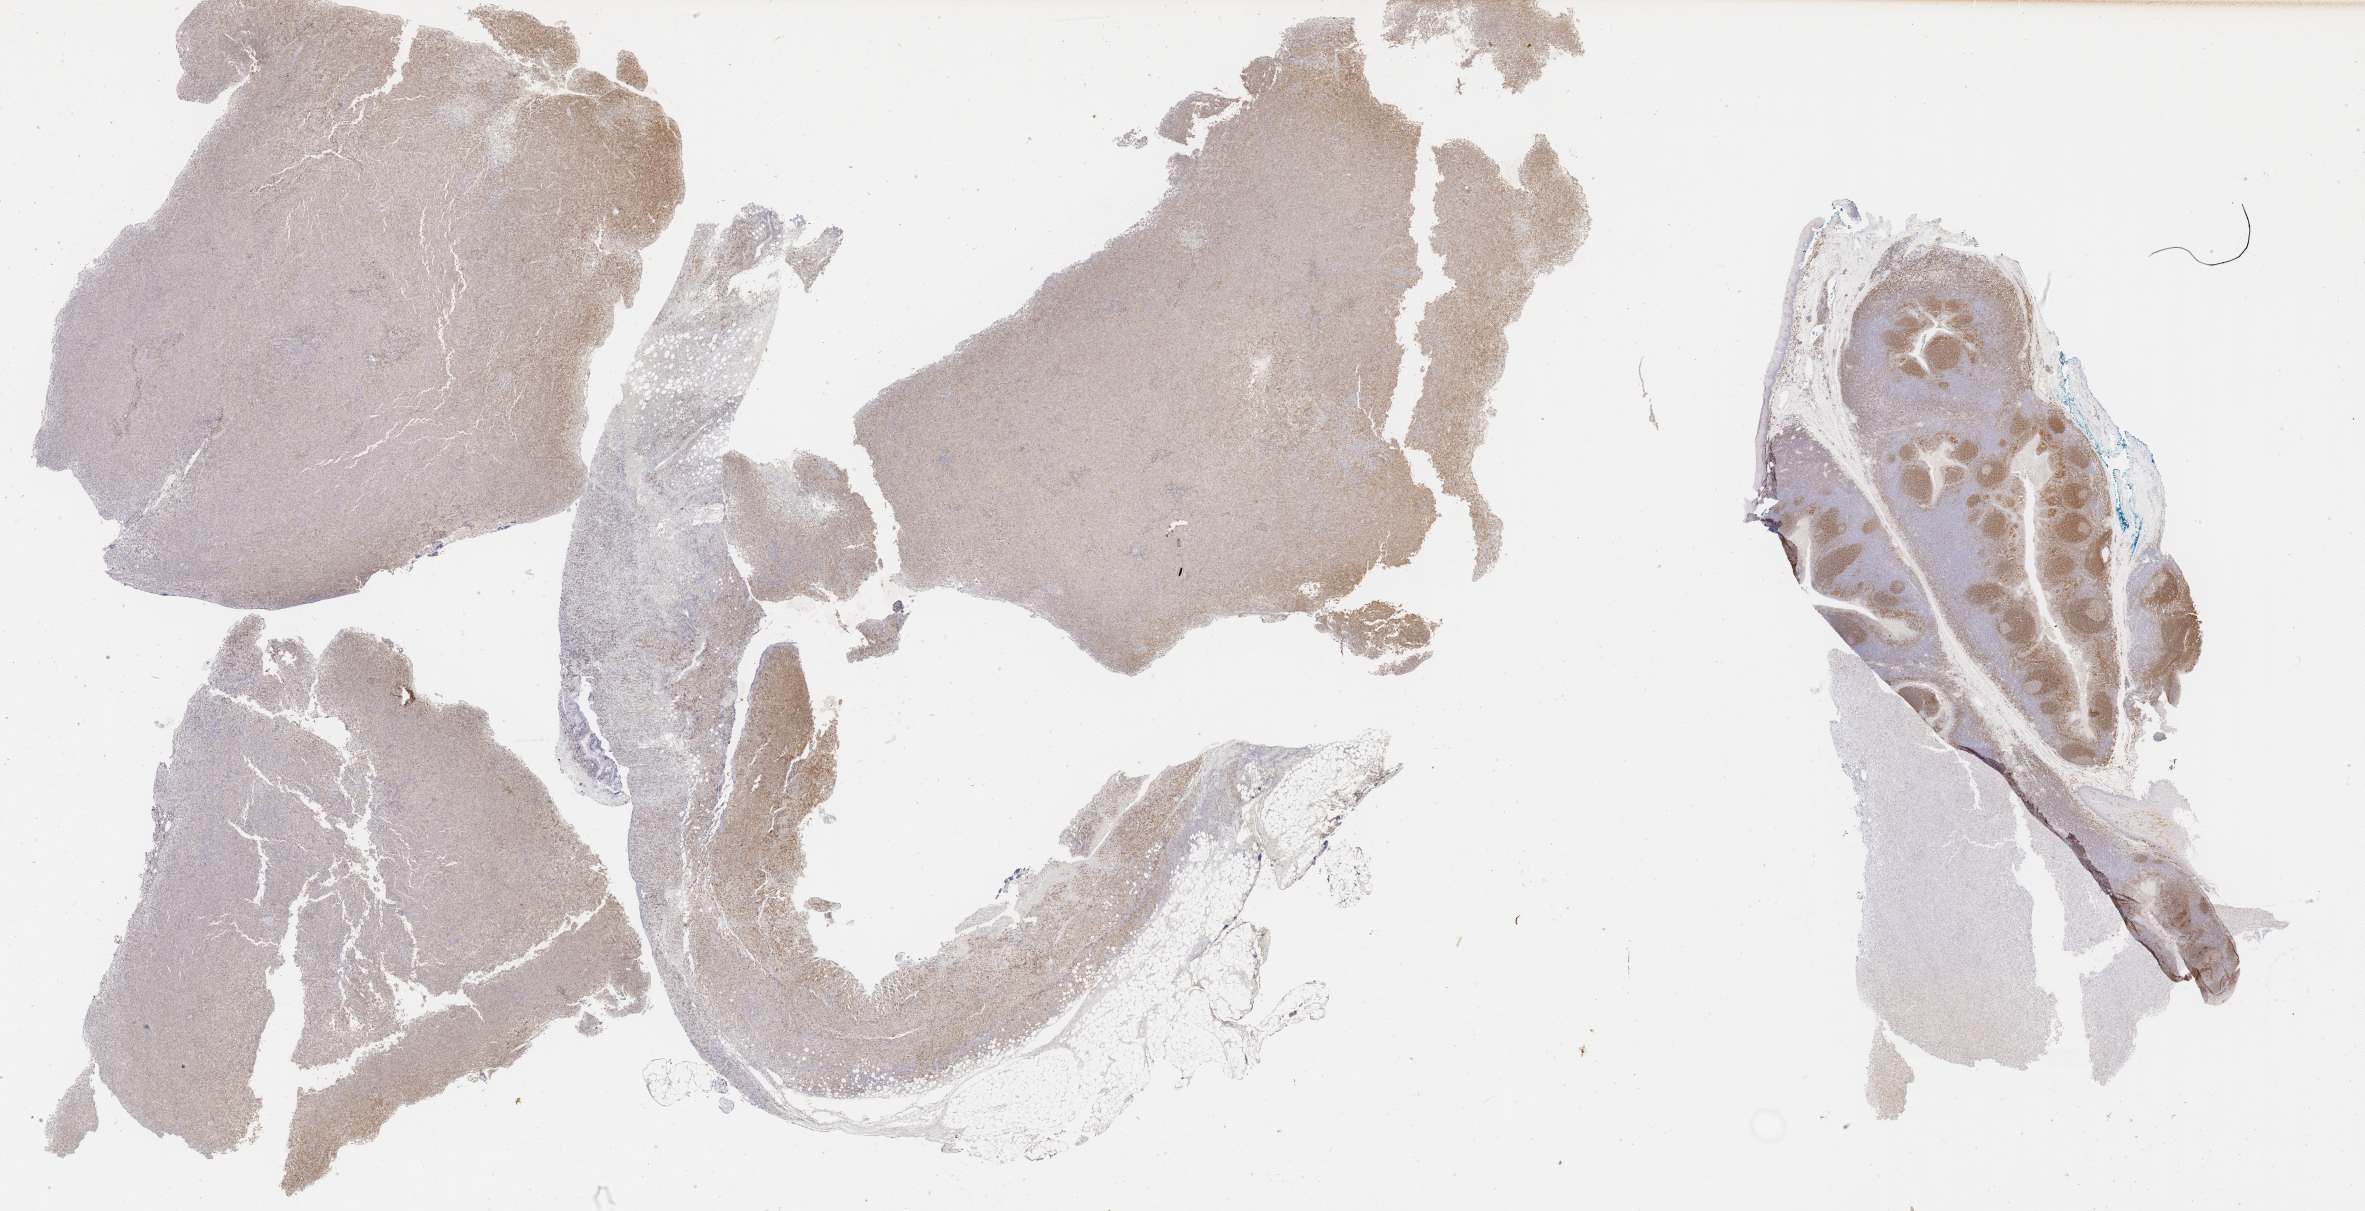
Whole-slide image, immunohistochemical stain for CD79a, a low-resolution overview of the entire scanned area, about 38.2 x 19.6 mm. Female patient.
Specimen: tumor tissue.